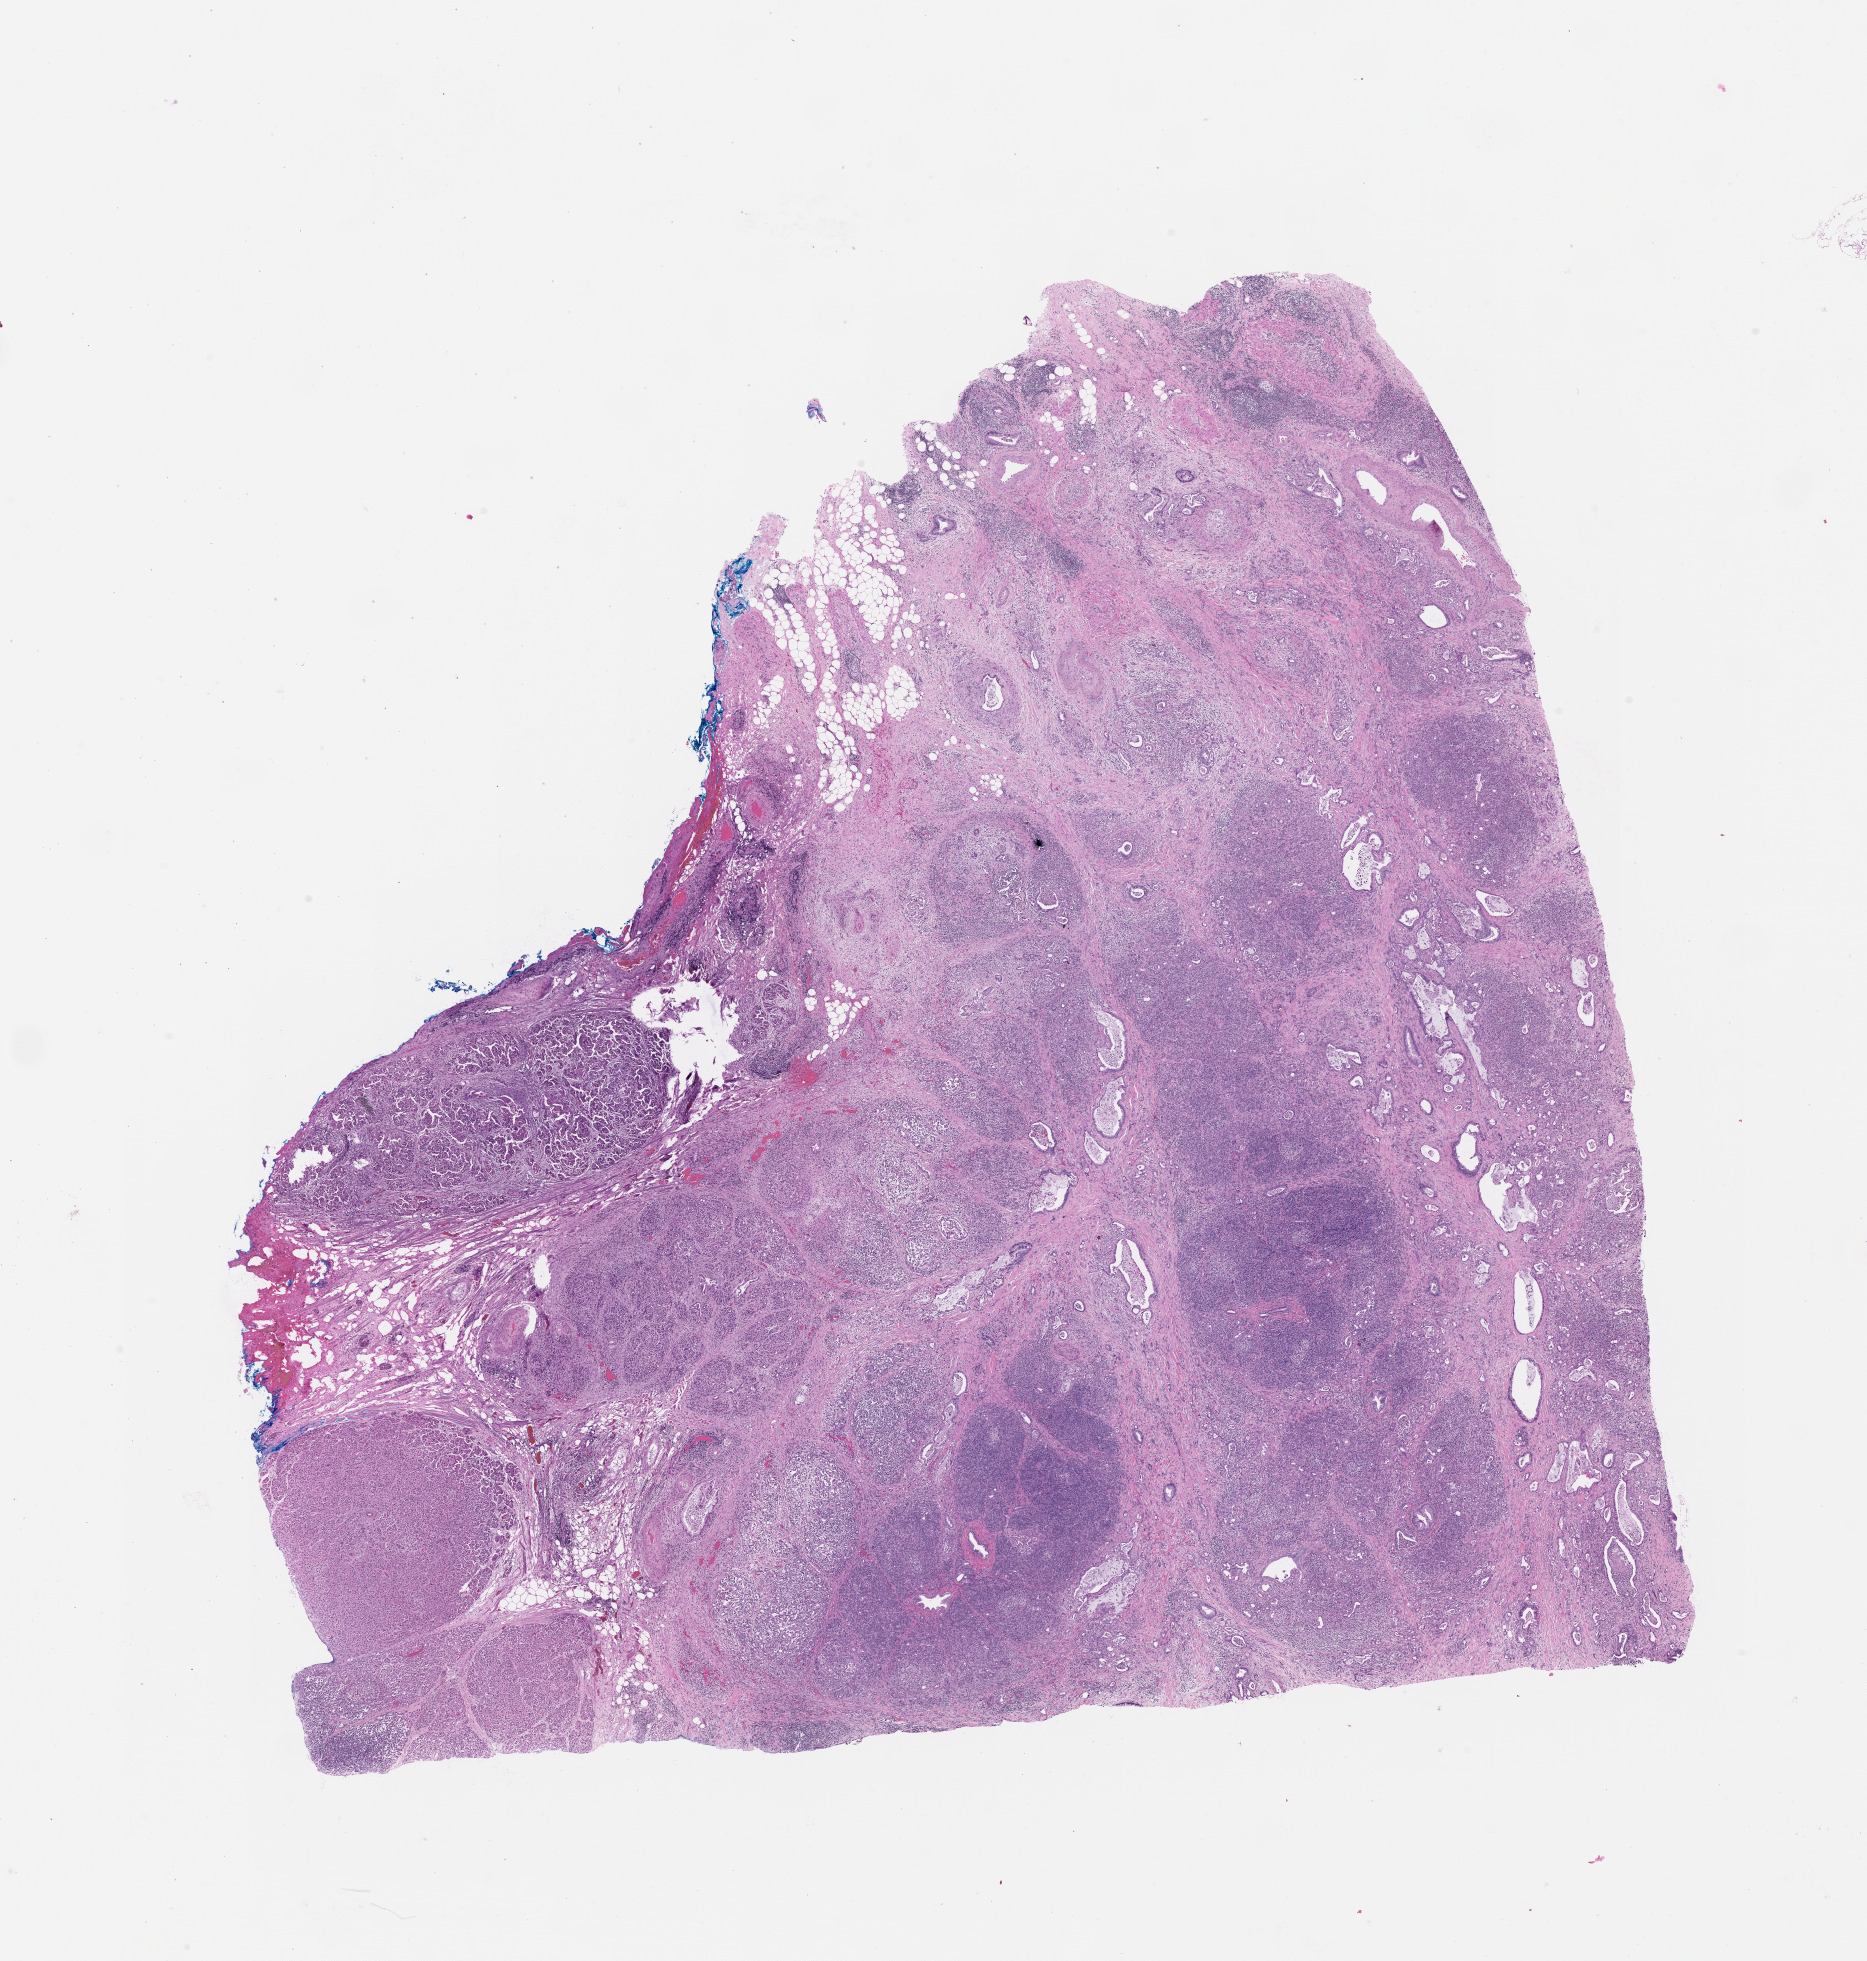
Digitized Hematoxylin and eosin (H&E) stained tissue section (whole slide) — a low-resolution overview of the entire scanned area, about 15.0 x 15.8 mm. Pancreas, tumour tissue. Male, 53 y/o.
Primary tumour site (as recorded): head. Patient diagnosis (cohort enrolment): ductal adenocarcinoma (pancreas).